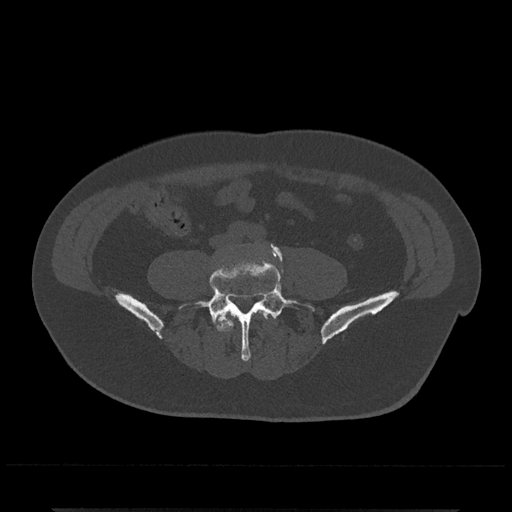
CT including the spine, one axial slice; slice 103 of 797 in the series (ordered by position); reconstruction kernel Br40s/3; bone window (W 1800 / L 400 HU); 0.5 mm slice thickness; 512 × 512 image matrix, field of view 393 × 393 mm. Male patient, age 67 years. Case-level facts recorded for this patient, not image findings: primary cancer: prostate.
Outlined on this slice (semi-automatic segmentation, software-assisted and operator-edited):
- L4 vertebra: box from (x=217, y=310) to (x=270, y=332) px
- L5 vertebra: (x=179, y=246)–(x=315, y=361)